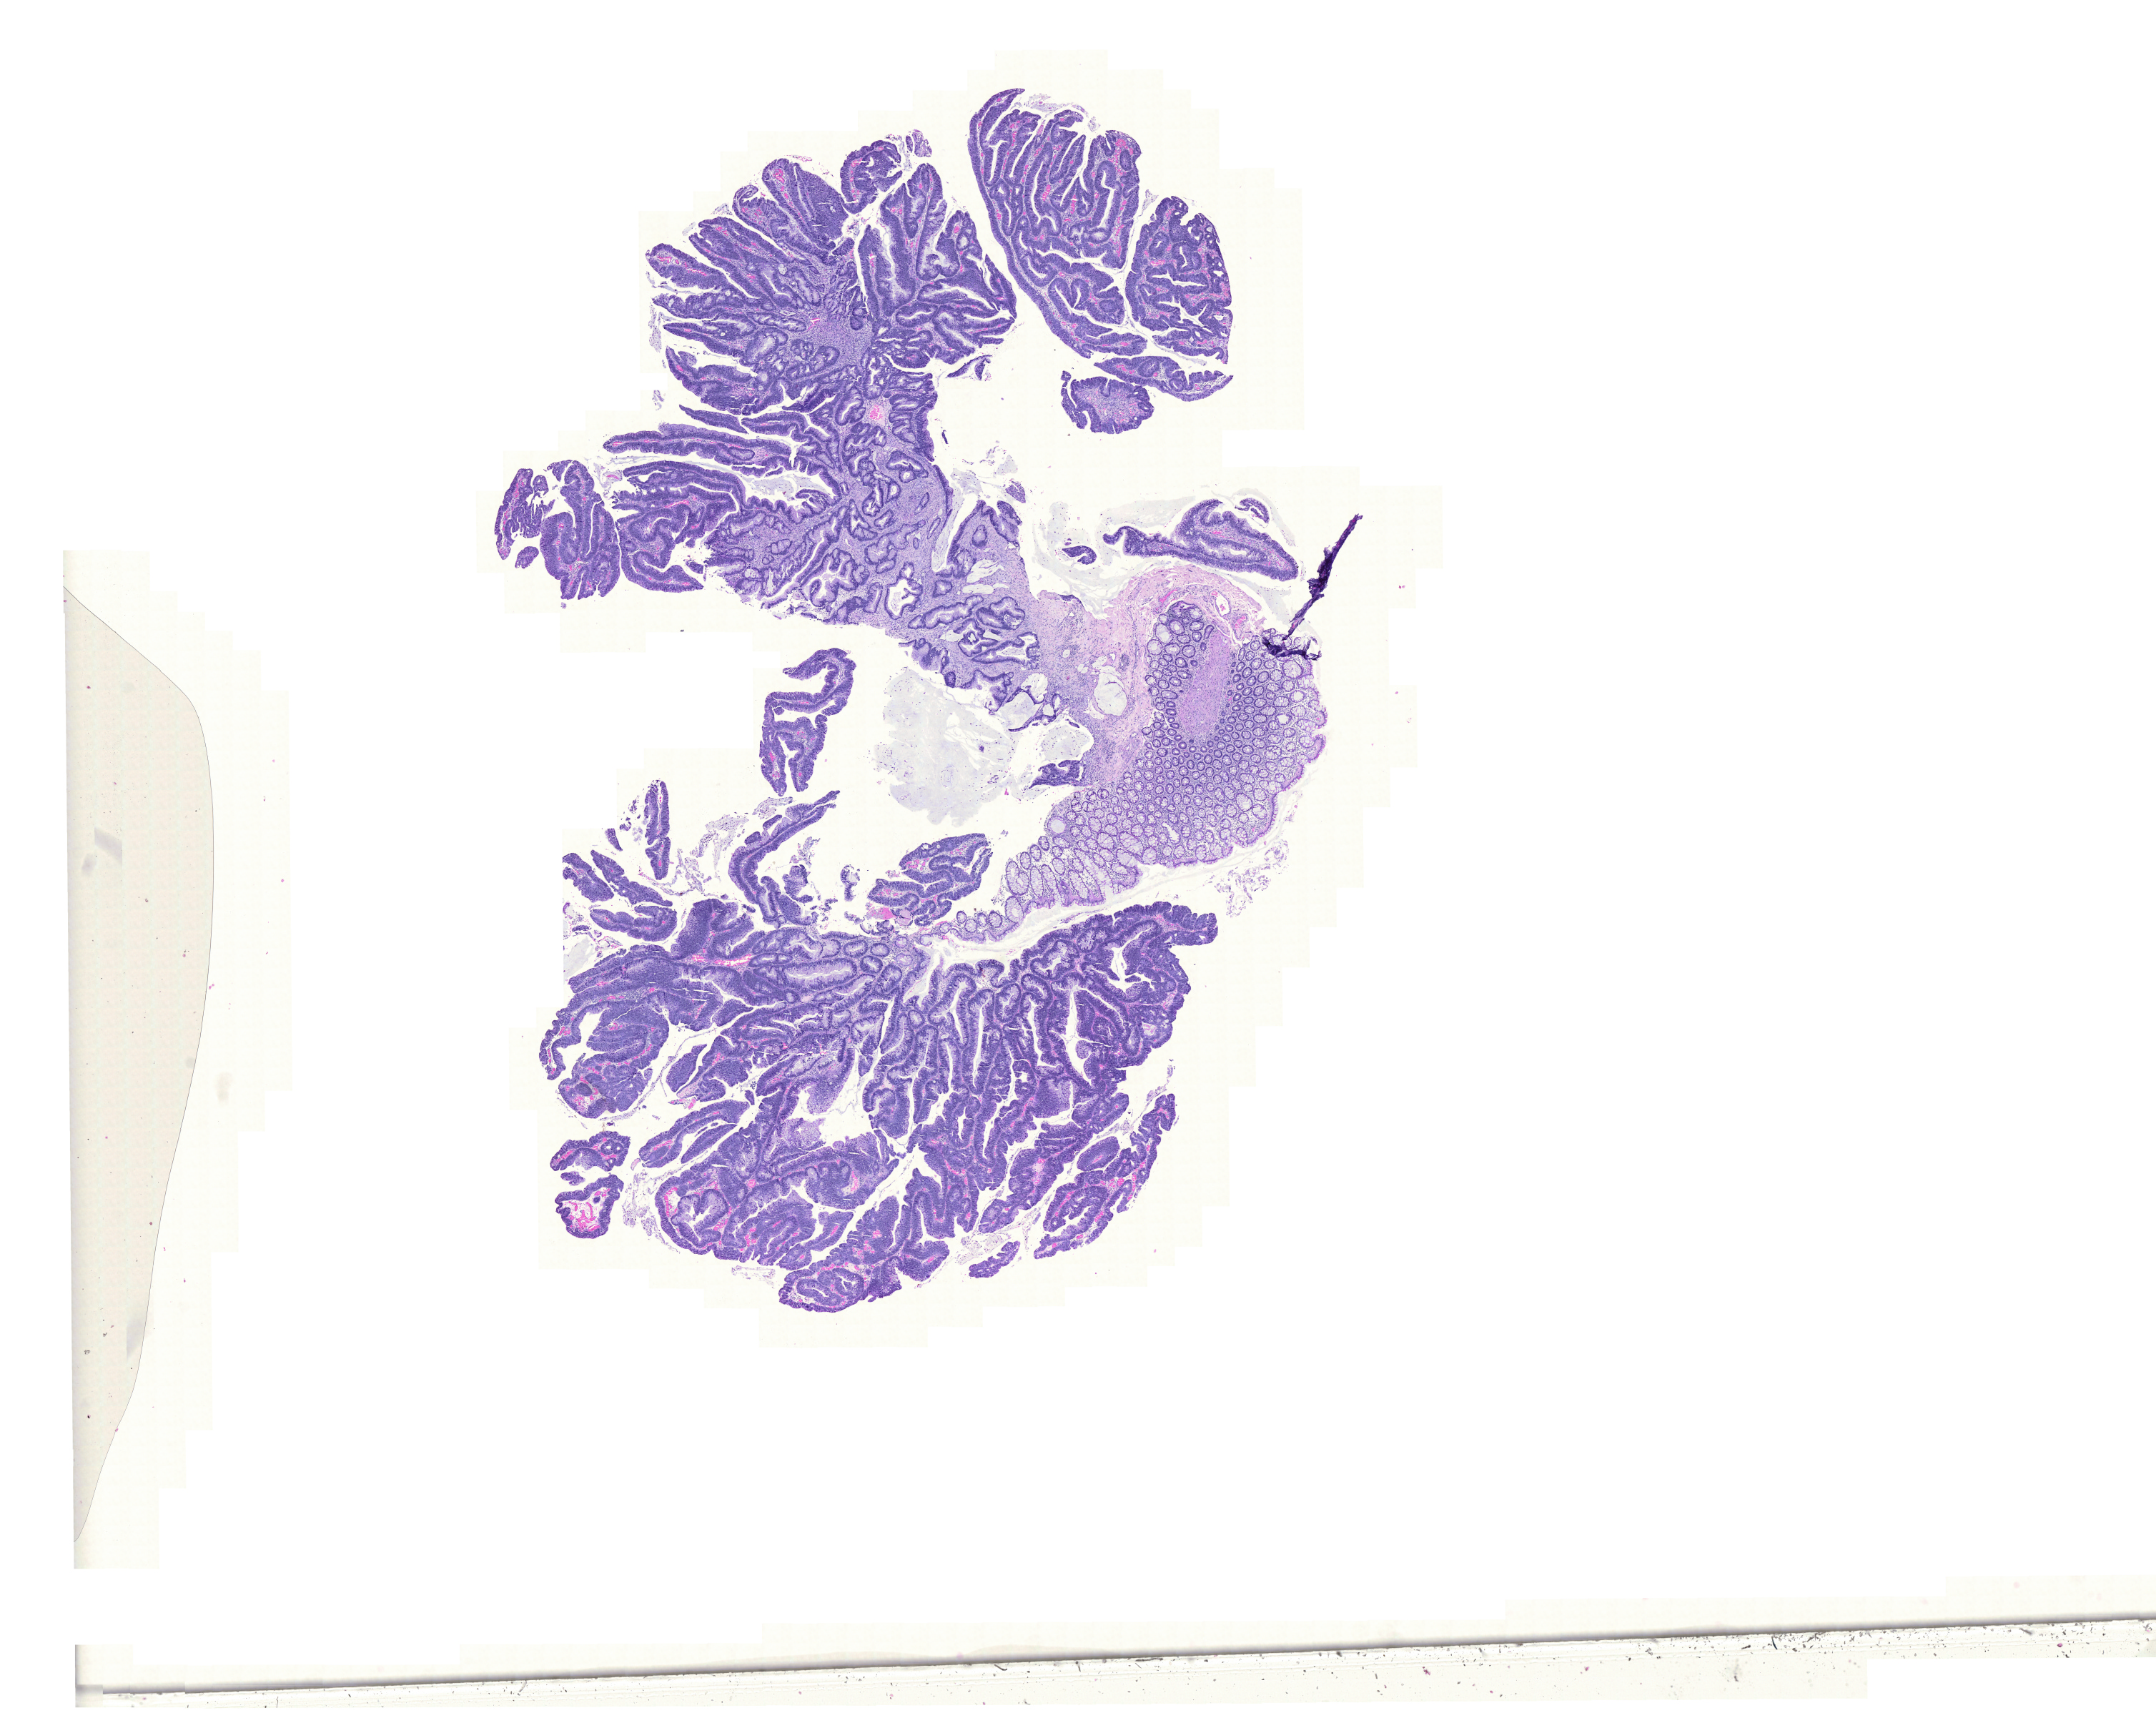
Digitized H&E tissue section (whole slide), a low-resolution overview of the entire scanned area, about 22.4 x 18.0 mm (acquisition: 20x scan), formalin-fixed paraffin-embedded (FFPE) diagnostic section, sample: primary tumour, rectum. Patient: female, age at initial diagnosis 50 years.
- TNM: T2 N0 M0
- AJCC pathologic stage: I (6th edition)
- pathologic diagnosis: Mucinous adenocarcinoma
- lymph nodes positive (case pathology): 0 of 28 examined